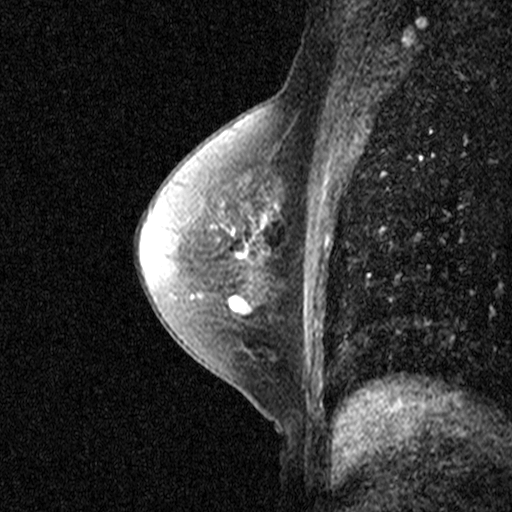
Breast MRI (dynamic contrast-enhanced), one sagittal slice; position 23 of 40 along the scan axis; dynamic contrast-enhanced study with each time point stored as its own series, time point 2 of 3 at this slice position (early post-contrast, ordered by acquisition time); 1.5 T; TE 4.5 ms, TR 11 ms; 512 × 512 image matrix, field of view 200 × 200 mm. Patient: female, 55 years. Case-level facts recorded for this patient, not image findings: setting: breast cancer imaged before/during neoadjuvant chemotherapy; receptor status: HR-positive, HER2-negative.
Structures marked on this image (semi-automatic segmentation, software-assisted and operator-edited):
- analysis volume of interest (the breast-tissue region the enhancement analysis was run in; not a lesion): bounding box [x1, y1, x2, y2] px = [194, 202, 279, 277]
- tumour enhancement mask (voxels above the 90 % enhancement threshold inside the analysis volume of interest): [243, 242, 247, 246]